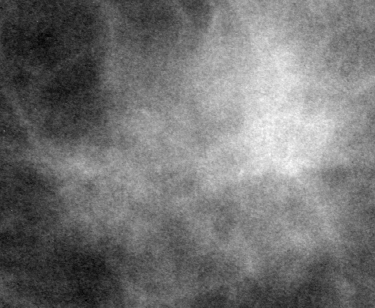
Region of interest cut from a scanned film mammogram (one marked finding), left breast, CC view.
- Mass, shape irregular, margins ill defined / spiculated; BI-RADS assessment category 4; subtlety rating 3 on a 1 (subtle) to 5 (obvious) scale; pathology (as recorded): malignant.